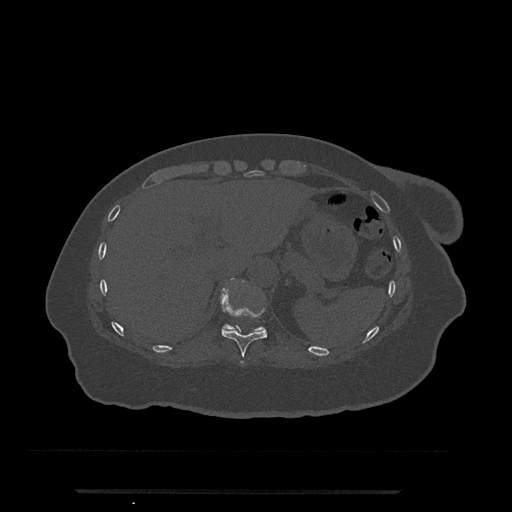
CT including the spine, one axial slice; position 270 of 797 along the scan axis; reconstruction kernel Br40s/3; bone window (W 1800 / L 400 HU); 512 × 512 image matrix, field of view 440 × 440 mm. Patient: female, 51 years. From the clinical record (not read from this slice): primary cancer: neuro; vertebrae with lytic lesions (as recorded): T8.
Annotated regions visible in this slice (semi-automatically segmented with operator editing):
- T10 vertebra: bounding box <220,278,267,365> (left, top, right, bottom; pixels)
- T11 vertebra: <224,325,263,331>